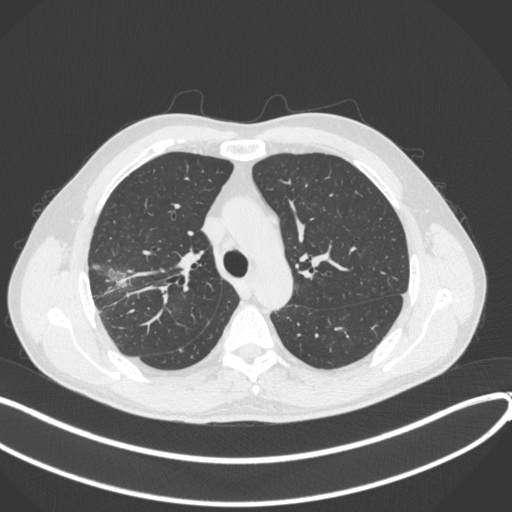
Chest CT, one axial slice. Position 297 of 381 along the scan axis. Reconstruction kernel B31f. 120 kVp. Lung window (W 1500 / L -600 HU). 512 × 512 image matrix, field of view 400 × 400 mm. Patient: male, 62 years. Case-level facts recorded for this patient, not image findings: clinical TNM (as recorded): T1c N0 M0.
Structures marked on this image (rectangle marked by the reading radiologist):
- lung tumour (recorded histology: adenocarcinoma): box from (x=102, y=264) to (x=129, y=293) px